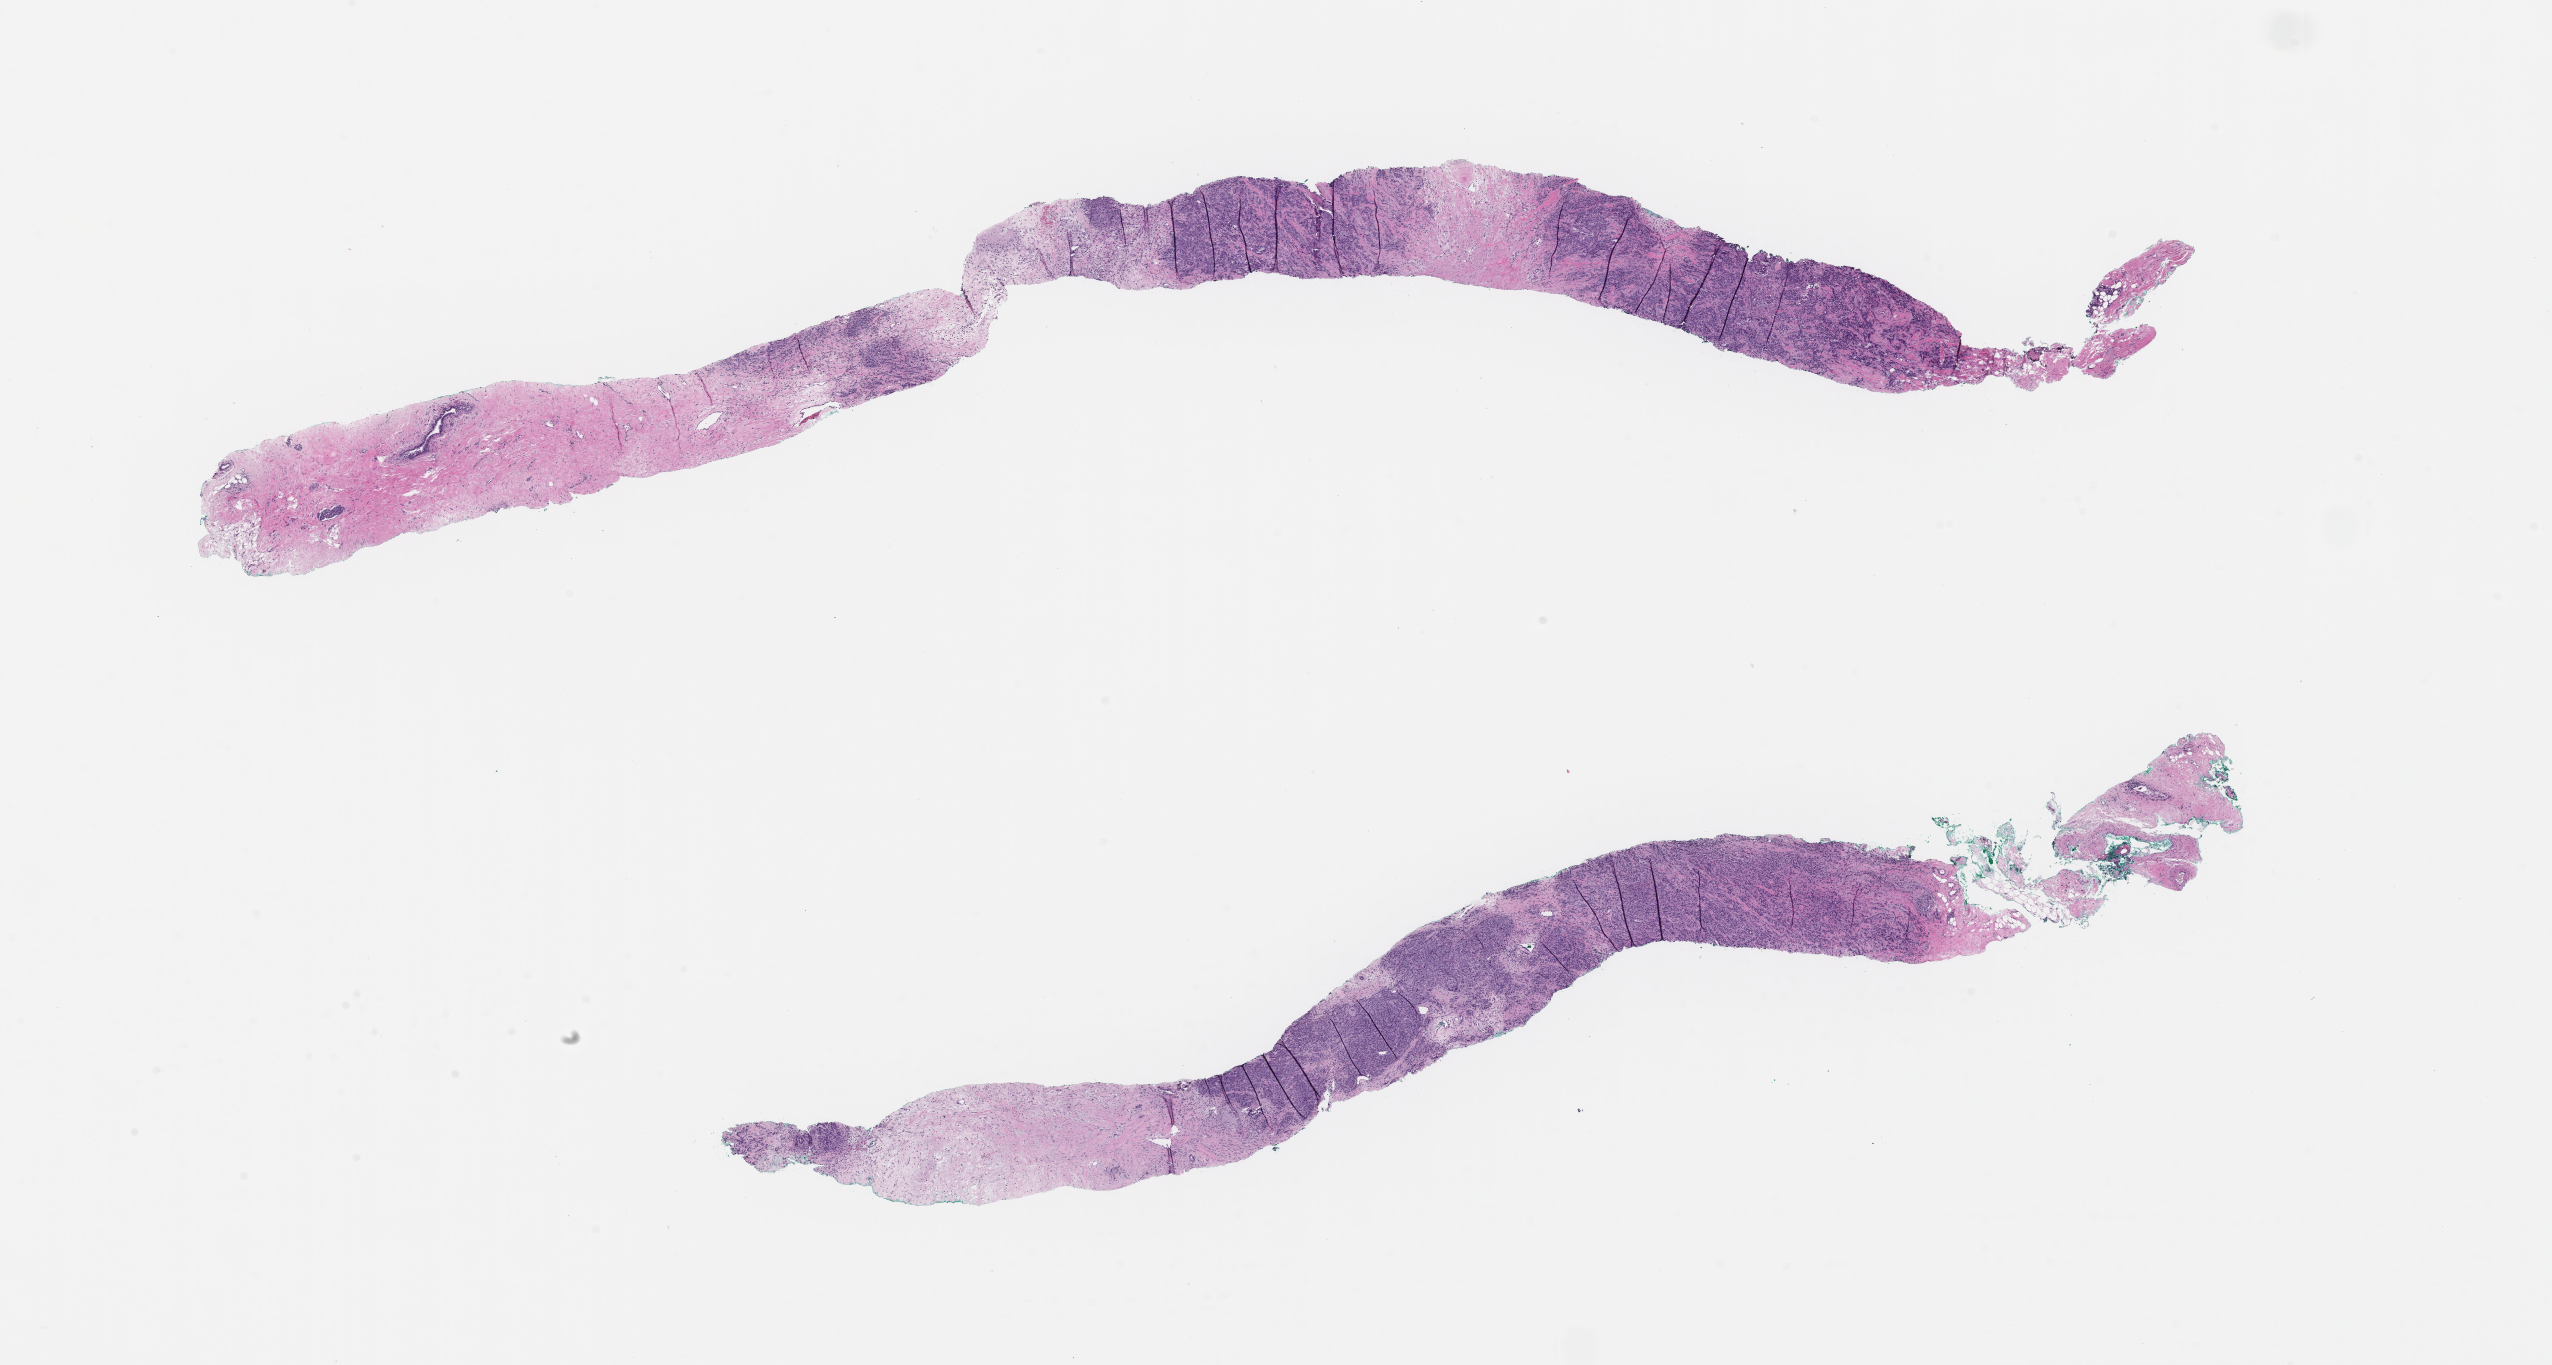
Haematoxylin and eosin whole-slide image — whole scanned area (about 20.6 x 11.0 mm) shown as a low-resolution overview. FFPE section. Site: breast. Archival tissue. Patient sex: female.
* this section: primary tumor
* diagnosis: Invasive Breast Carcinoma